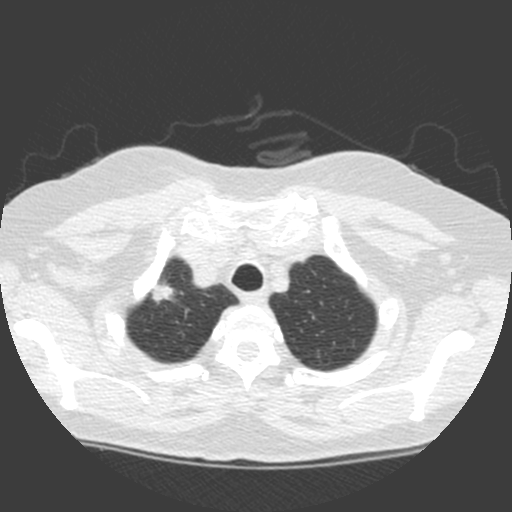
Low-dose screening chest CT, one axial slice; position 142 of 155 along the scan axis; 120 kVp; lung window (W 1500 / L -600 HU); 512 × 512 image matrix.
Outlined on this slice (expert manual segmentation):
- lesion 1 (tumor, upper lobe of right lung): box from (x=150, y=282) to (x=174, y=304) px